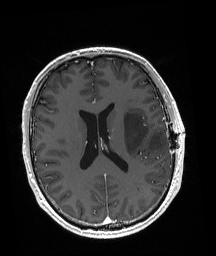
Brain MRI from a brain-tumour surgery series, one axial slice. Slice 83 of 192 in the series (ordered by position). T1-weighted post-contrast. 1 mm slice thickness. 216 × 256 image matrix, field of view 211 × 250 mm. From the clinical record (not read from this slice): histopathology: Astrocytoma; WHO grade: 3; IDH mutation: yes.
Outlined on this slice (expert manual segmentation):
- tumour: bounding box <123,112,167,156> (left, top, right, bottom; pixels)